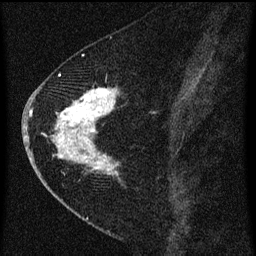
Breast MRI (dynamic contrast-enhanced), one sagittal slice; position 28 of 60 along the scan axis; dynamic contrast-enhanced series, image 2 of 3 at this slice position (ordered by acquisition); 1.5 T; TE 4.2 ms, TR 8 ms; 256 × 256 image matrix, field of view 180 × 180 mm. Female patient, age 47 years.
Structures marked on this image (semi-automatically segmented with operator editing):
- analysis volume of interest (the breast-tissue region the enhancement analysis was run in; not a lesion): bounding box (x1, y1, x2, y2) in pixels: (38, 76, 127, 193)
- tumour enhancement mask (voxels above the 70 % enhancement threshold inside the analysis volume of interest): (45, 76, 118, 177)